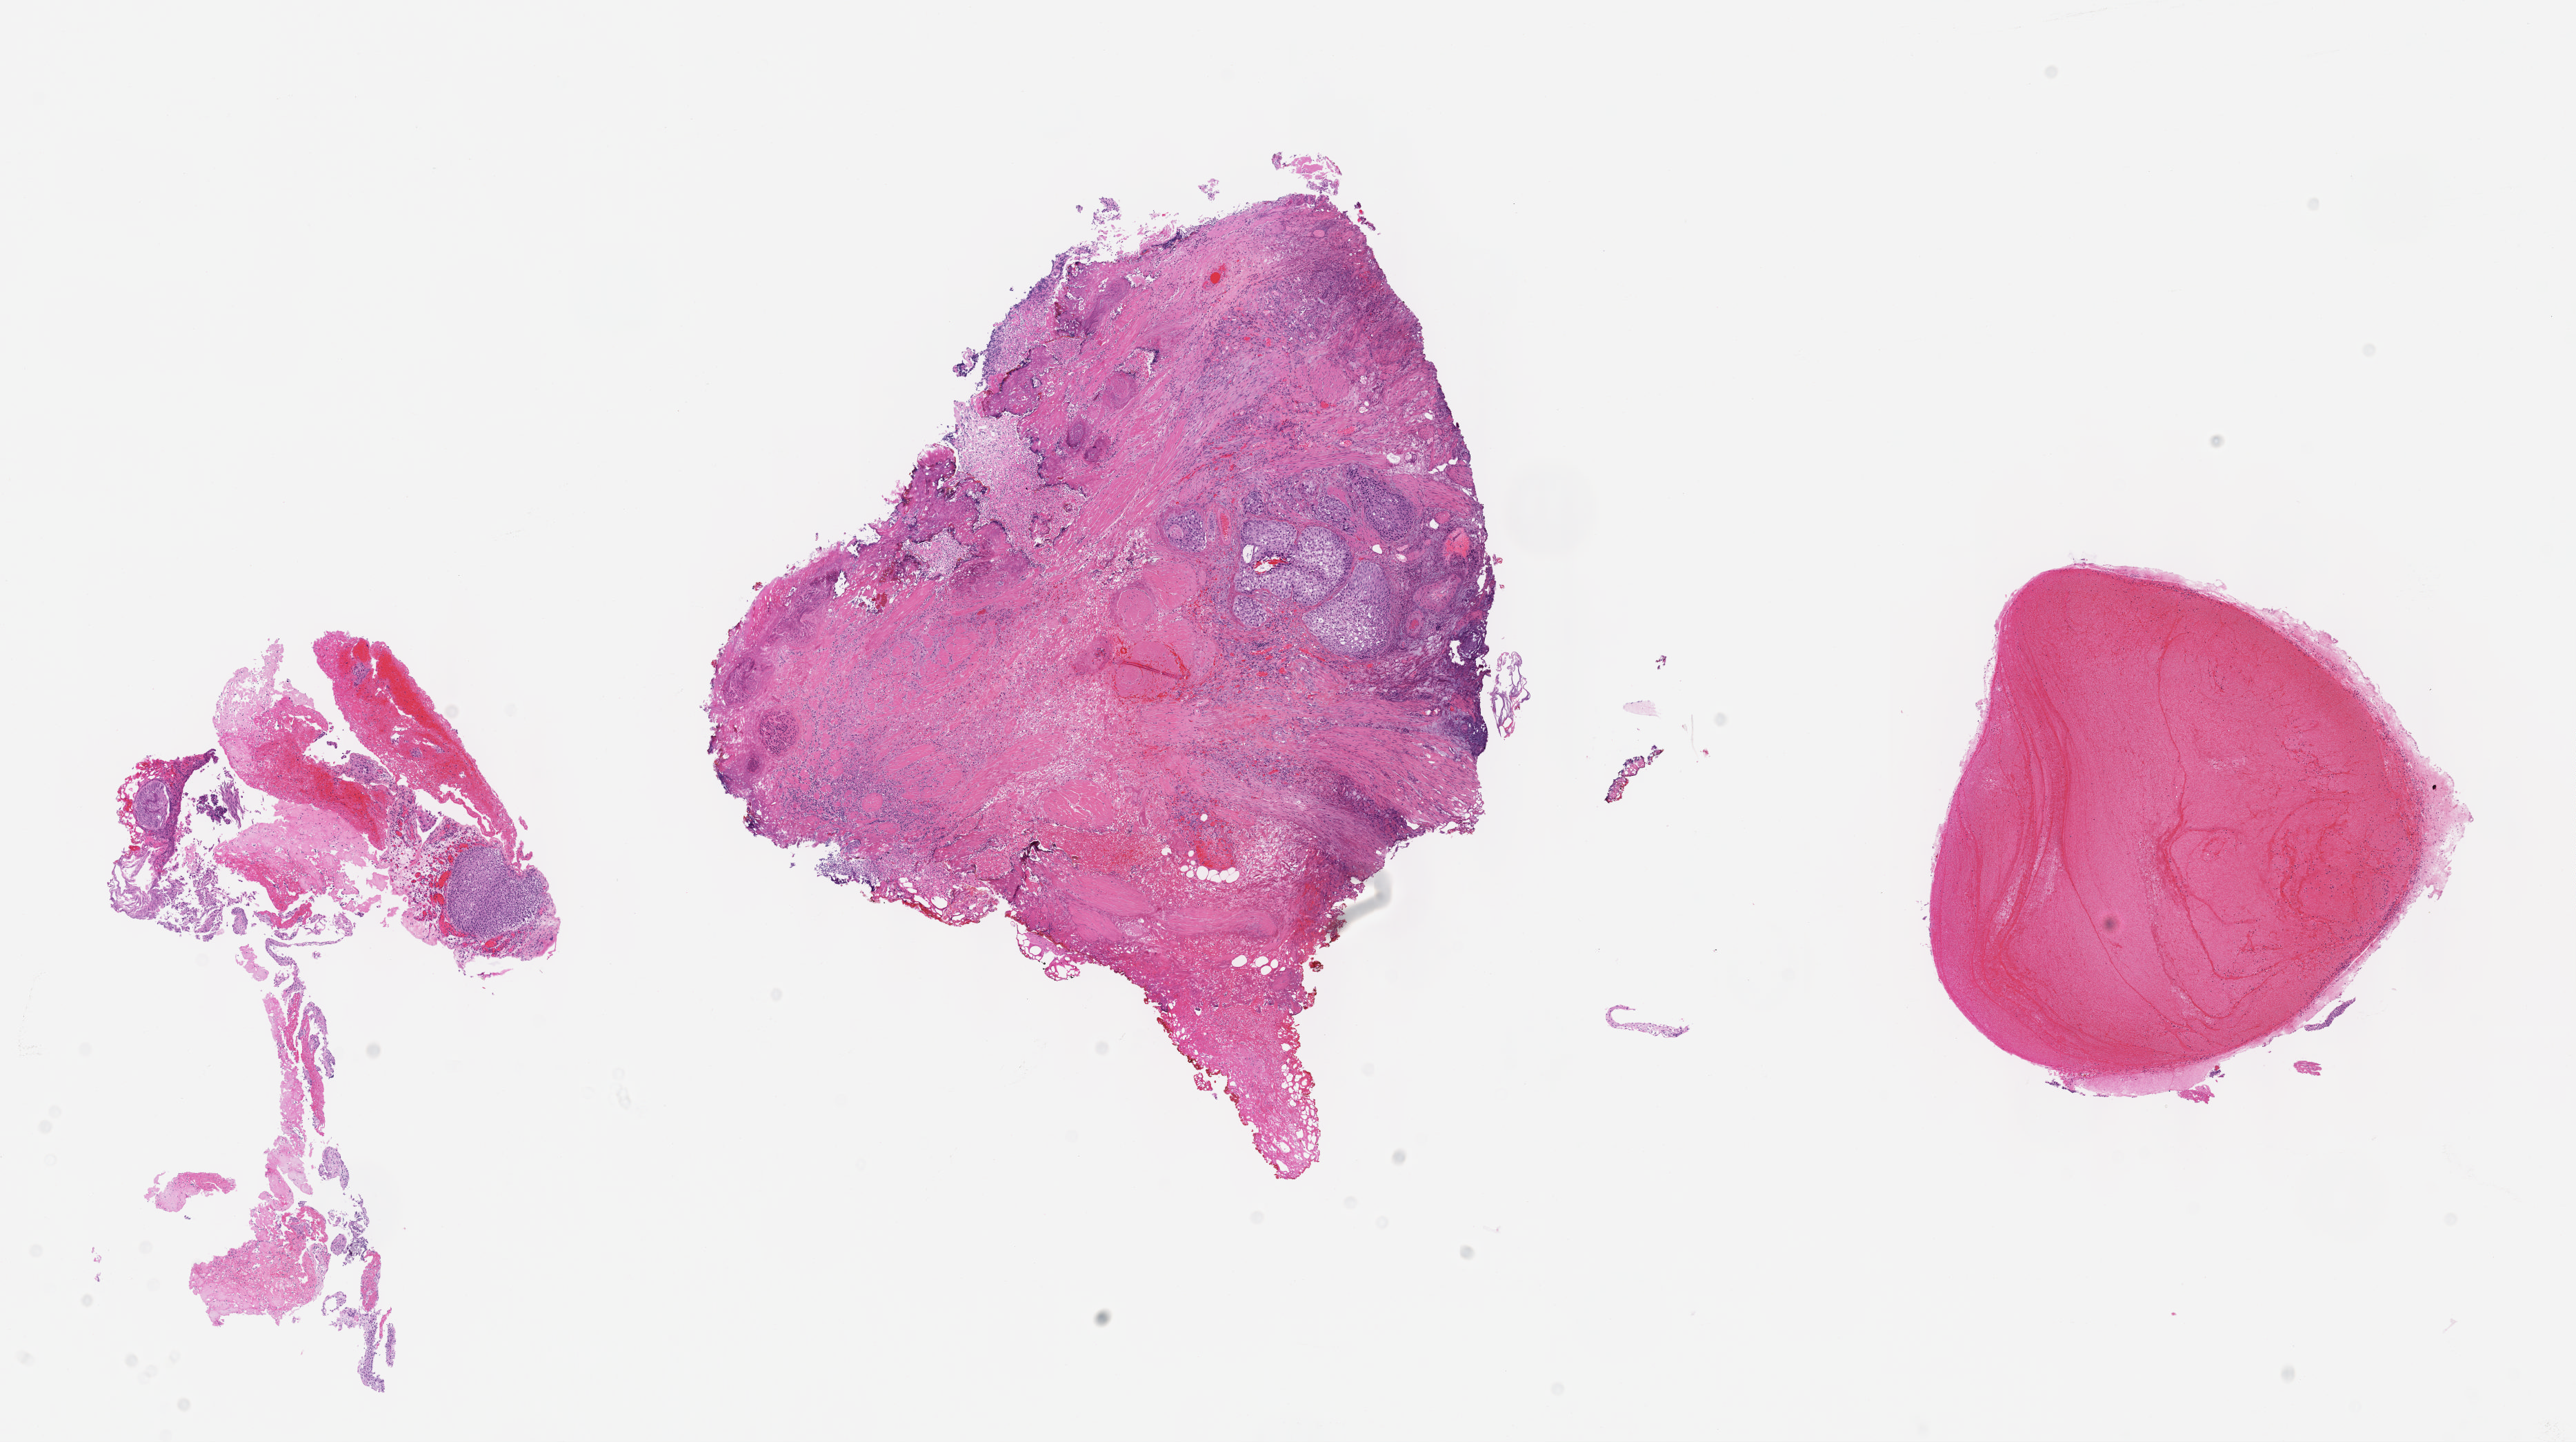
H&E whole-slide image, whole scanned area (about 15.1 x 8.4 mm) shown as a low-resolution overview; formalin-fixed paraffin-embedded (FFPE) diagnostic section; primary tumour sample from the bladder. Patient: male, age at initial diagnosis 60 years. Histologic grade: high grade.
AJCC pathologic stage: IV (6th edition). Lymph nodes positive (case pathology): 2 of 27 examined. Histologic diagnosis: Transitional cell carcinoma.